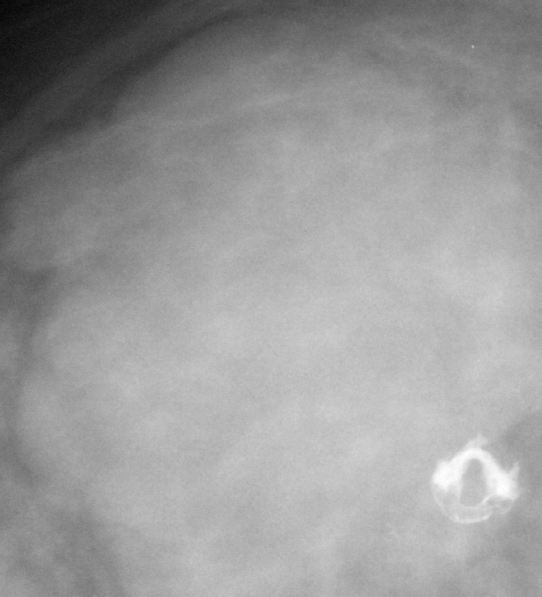
Region of interest cut from a scanned film mammogram (one marked finding); right breast; CC view.
Mass, shape round, margins microlobulated; BI-RADS assessment category 4; subtlety rating 5 on a 1 (subtle) to 5 (obvious) scale; pathology (as recorded): benign.